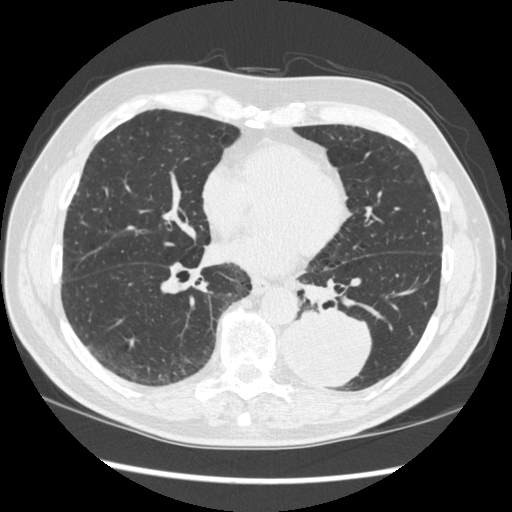
Low-dose screening chest CT, one axial slice; slice 139 of 348 in the series (ordered by position); reconstruction kernel STANDARD; 120 kVp; lung window (W 1500 / L -600 HU); 512 × 512 image matrix, field of view 360 × 360 mm.
Annotated regions visible in this slice (manually delineated by an expert):
- lesion 1 (tumor, lower lobe of left lung): bounding box (x1, y1, x2, y2) in pixels: (283, 310, 372, 387)